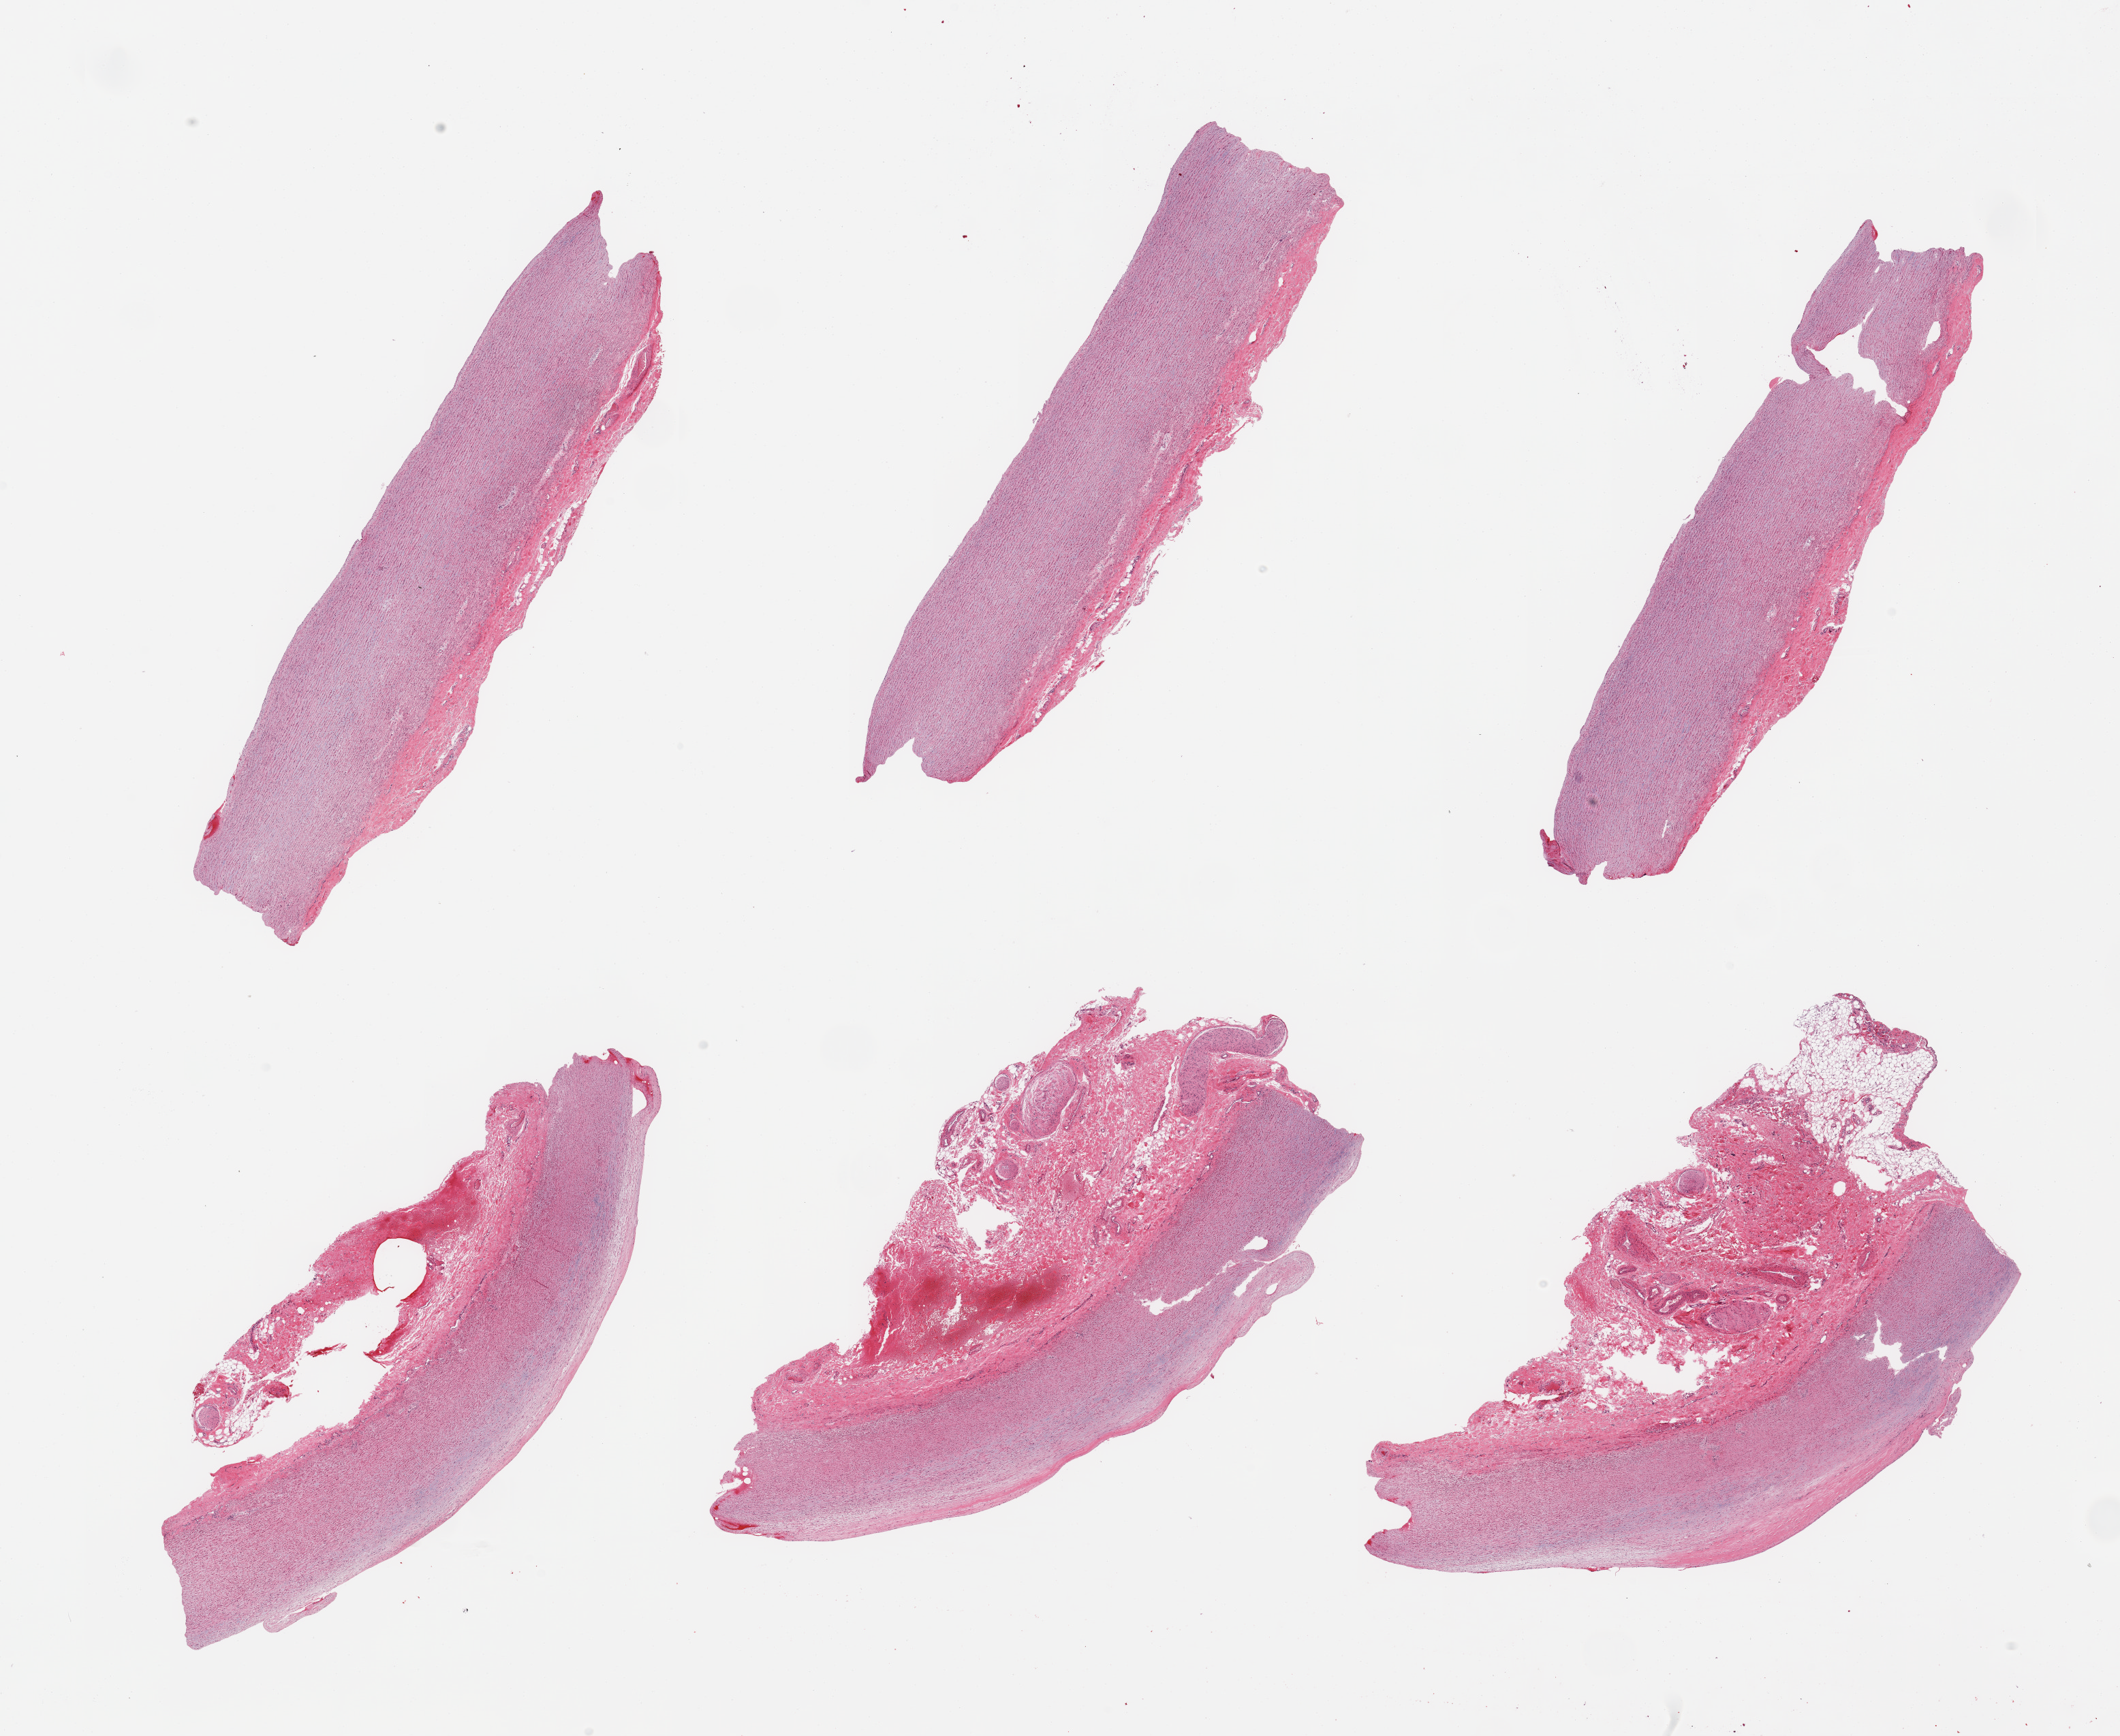
Haematoxylin and eosin whole-slide image — whole scanned area (about 24.6 x 20.2 mm) shown as a low-resolution overview, PAXgene-fixed paraffin-embedded (PFPE) section, sampled site (target tissue): aorta, tissue donor sample.
• review note (as recorded): 6 pieces, no significant atherosis, adherent serosa/fat/peripheral nerve elments up to ~3mm